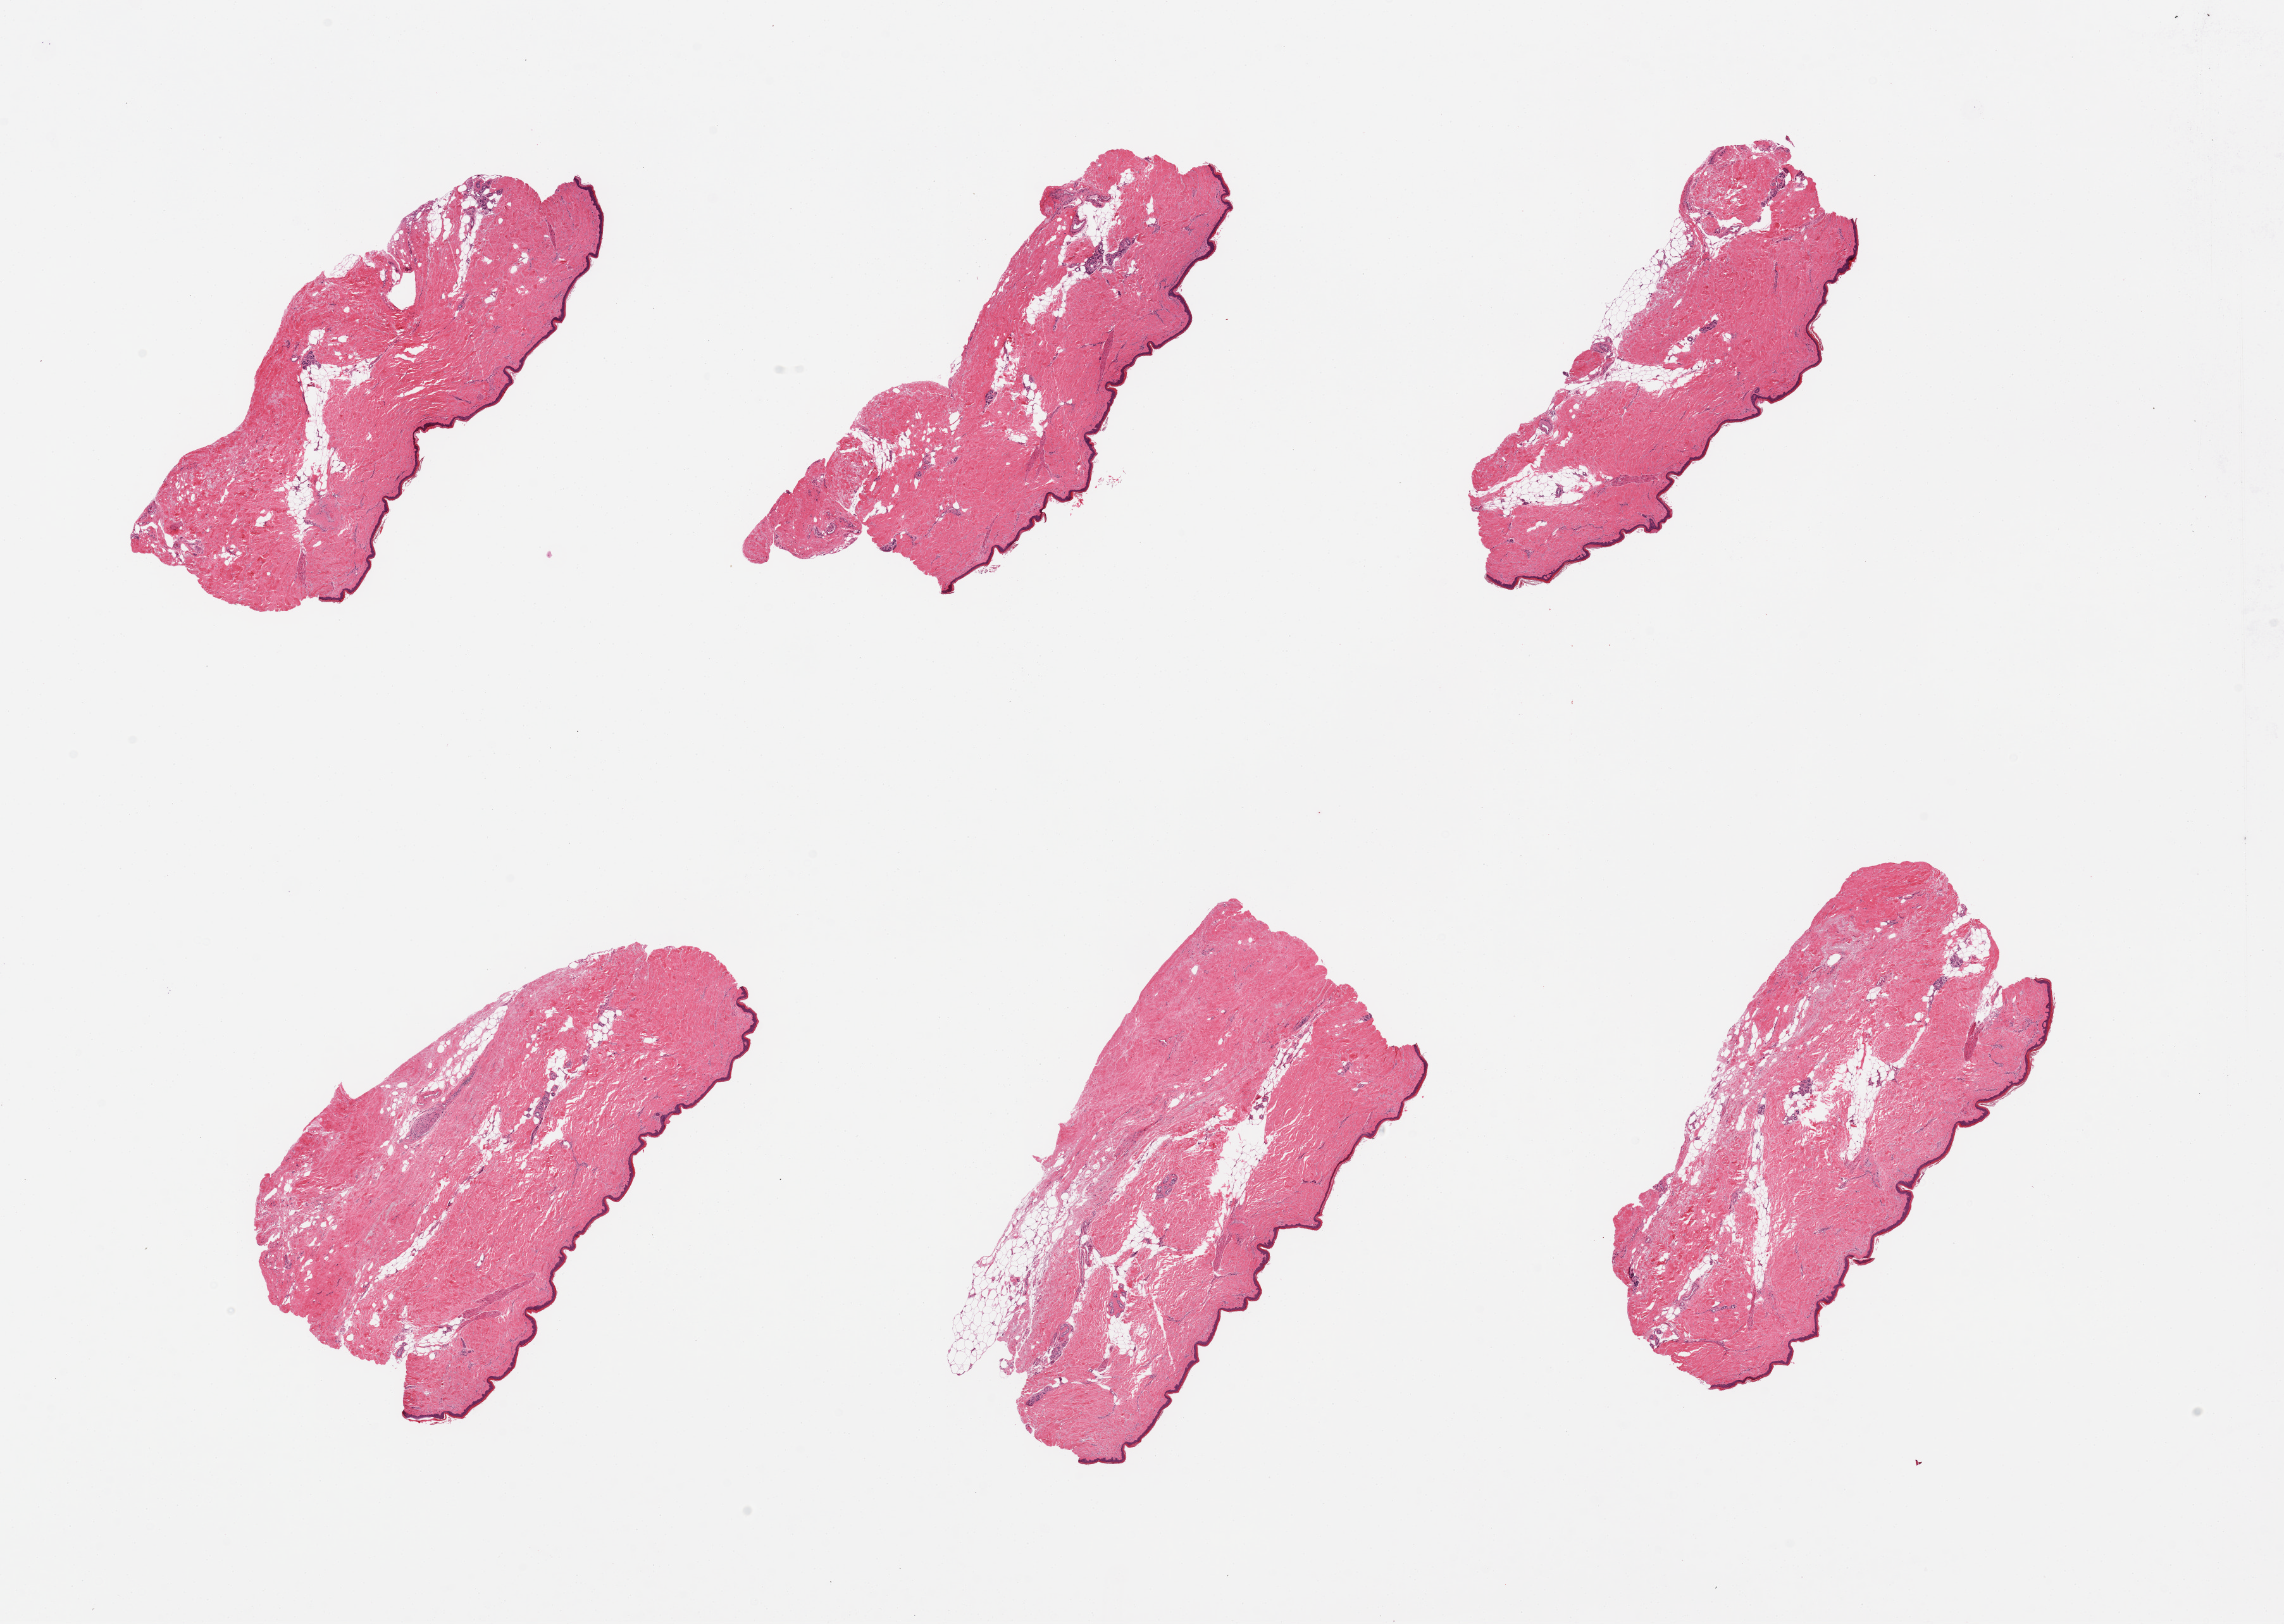
Whole-slide image, hematoxylin and eosin (H&E) stain — a low-resolution overview of the entire scanned area, about 28.5 x 20.3 mm, PAXgene-fixed, paraffin-embedded tissue, target tissue: skin of lower leg, donor tissue sample. Donor: male.
Review note (as recorded): 6 pieces, minimal attached and internal fat (<10%).